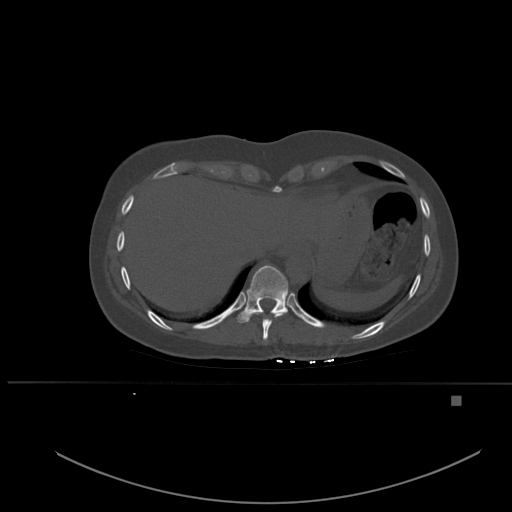
CT including the spine, one axial slice; bone window (W 1800 / L 400 HU); 1.5 mm slice thickness; 512 × 512 image matrix, field of view 443 × 443 mm. Patient: female, 49 years. From the clinical record (not read from this slice): primary cancer: breast; vertebrae with lytic lesions (as recorded): L3, T12, L4.
Structures marked on this image (semi-automatic segmentation, software-assisted and operator-edited):
- T10 vertebra: bounding box (x1, y1, x2, y2) in pixels: (237, 265, 288, 323)
- T9 vertebra: (250, 311, 288, 341)